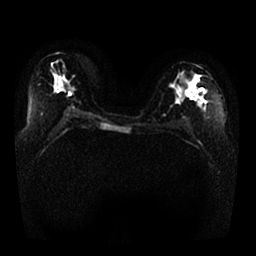
Breast MRI, one axial slice. Position 15 of 25 along the scan axis. Diffusion-weighted series; image 2 of 4 stored at this slice position (different b-values; order by instance number). 1.5 T. 4 mm slice thickness. 256 × 256 image matrix, field of view 350 × 350 mm. Female patient.
Outlined on this slice (outlined manually by an expert reader):
- tumour on diffusion-weighted imaging: bounding box (x1, y1, x2, y2) in pixels: (186, 87, 195, 98)